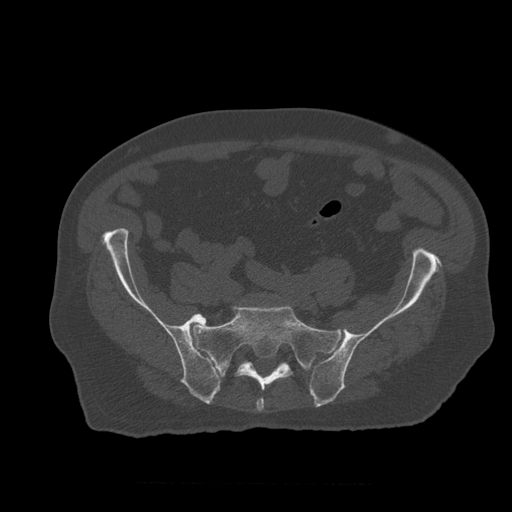
CT including the spine, one axial slice. Slice 117 of 399 in the series (ordered by position). 120 kVp. Bone window (W 1800 / L 400 HU). 512 × 512 image matrix, field of view 407 × 407 mm. Patient age 73 years. Case-level facts recorded for this patient, not image findings: primary cancer: prostate; vertebrae with lytic lesions (as recorded): L2.
Annotated regions visible in this slice (semi-automatic segmentation, software-assisted and operator-edited):
- L5 vertebra: bounding box <213,367,219,375> (left, top, right, bottom; pixels)